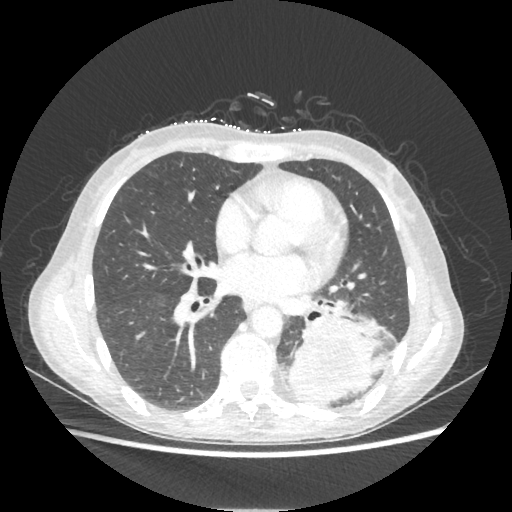
Chest CT, one axial slice. Slice 104 of 221 in the series (ordered by position). Reconstruction kernel STANDARD. Lung window (W 1500 / L -600 HU). 1.25 mm slice thickness. 512 × 512 image matrix, field of view 360 × 360 mm. Patient: female, 53 years. Case-level facts recorded for this patient, not image findings: clinical TNM (as recorded): T3 N0 M0.
Annotated regions visible in this slice (bounding box drawn by a radiologist):
- lung tumour (recorded histology: adenocarcinoma): box from (x=283, y=310) to (x=382, y=404) px